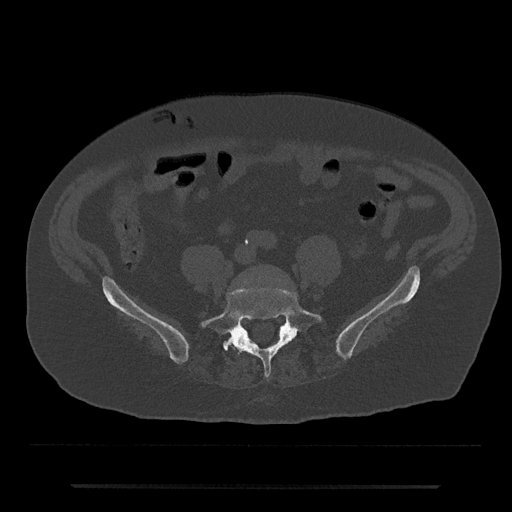
CT including the spine, one axial slice; slice 294 of 797 in the series (ordered by position); bone window (W 1800 / L 400 HU); 0.5 mm slice thickness; 512 × 512 image matrix, field of view 434 × 434 mm. Male patient, age 80 years. From the clinical record (not read from this slice): primary cancer: prostate; vertebrae with lytic lesions (as recorded): L1, T11.
Structures marked on this image (semi-automatic segmentation, software-assisted and operator-edited):
- L5 vertebra: bounding box (x1, y1, x2, y2) in pixels: (201, 287, 322, 378)